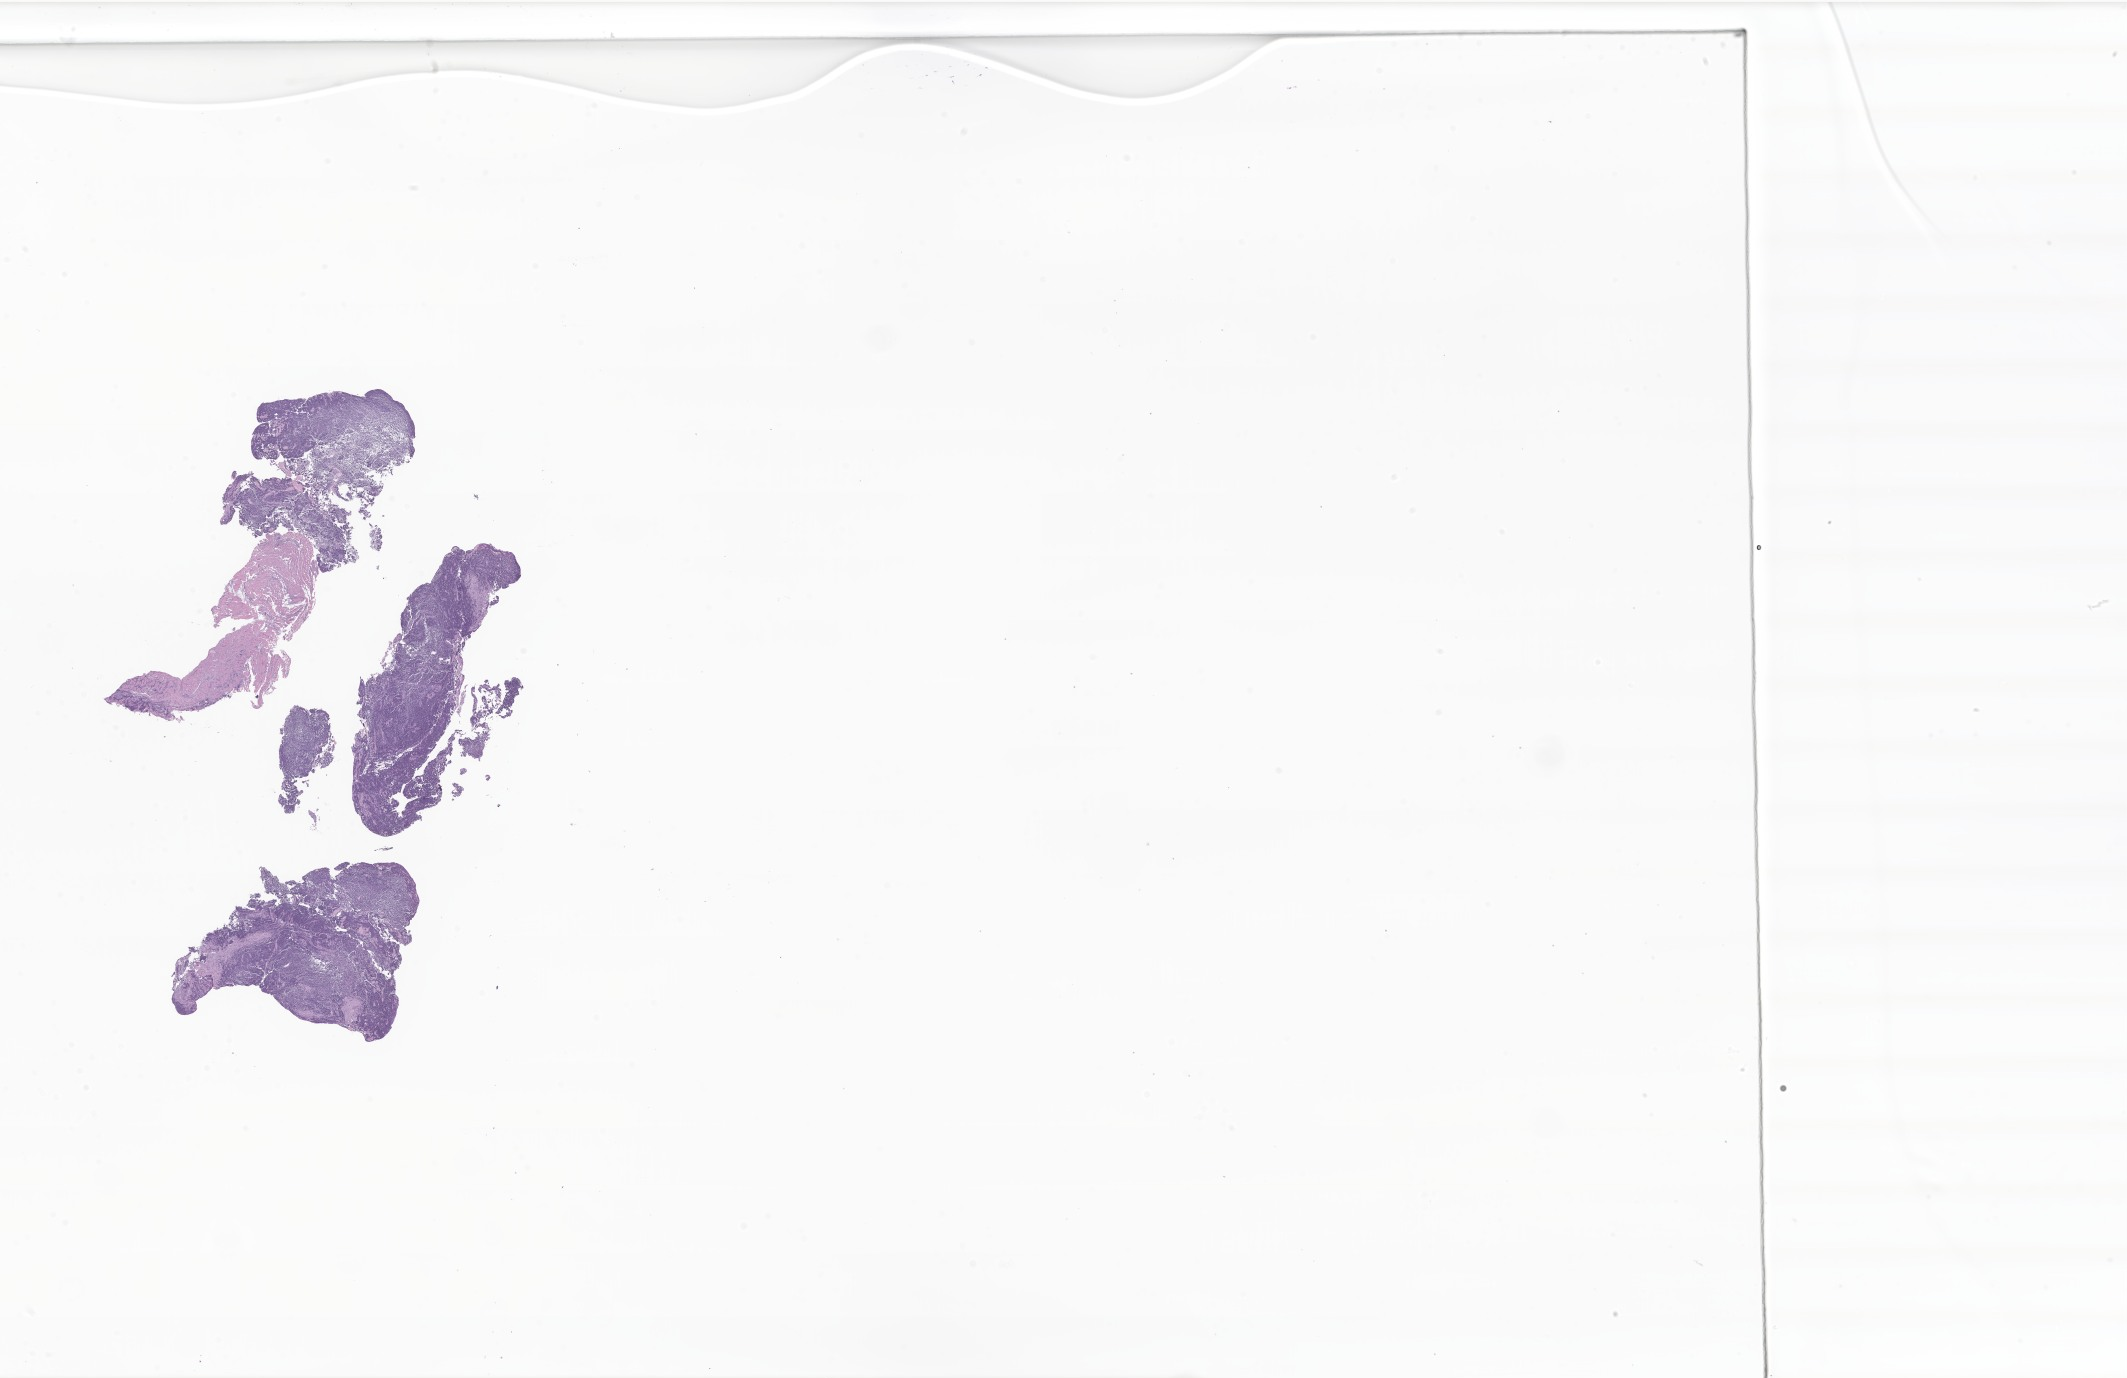
Whole-slide image, haematoxylin and eosin stain of tumor tissue from the soft tissues of head and neck — whole scanned area (about 35.9 x 23.2 mm) shown as a low-resolution overview, formalin-fixed, paraffin-embedded (FFPE) tissue. Patient: male, age 48 months (4 years).
Diagnosis: Rhabdomyosarcoma, NOS. Tissue or organ of origin (case record): connective, subcutaneous and other soft tissues of head, face, and neck.